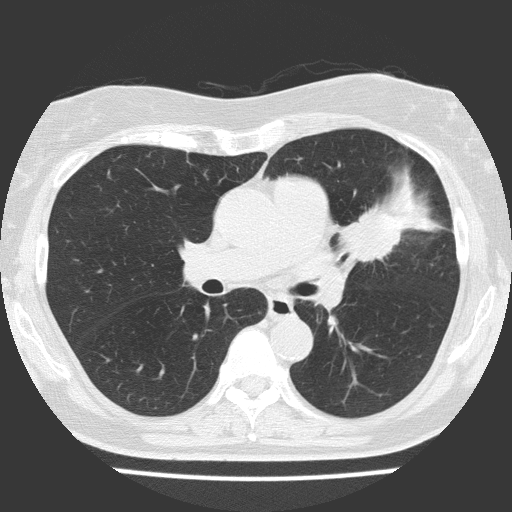
Low-dose screening chest CT, one axial slice; slice 85 of 151 in the series (ordered by position); 120 kVp; lung window (W 1500 / L -600 HU); 2 mm slice thickness; 512 × 512 image matrix, field of view 309 × 309 mm.
Annotated regions visible in this slice (expert manual segmentation):
- lesion 1 (tumor, upper lobe of left lung): box from (x=341, y=206) to (x=403, y=262) px